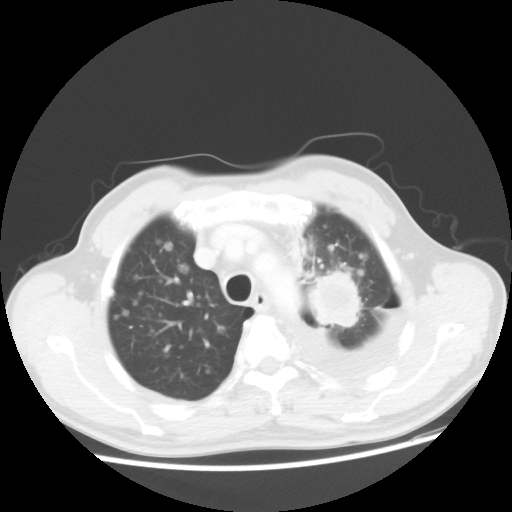
Chest CT, one axial slice. Slice 38 of 48 in the series (ordered by position). 100 kVp. Lung window (W 1500 / L -600 HU). 512 × 512 image matrix, field of view 362 × 362 mm. Patient: male, 55 years. From the clinical record (not read from this slice): clinical TNM (as recorded): T2 N3 M1a; histopathological grade: G3.
Outlined on this slice (rectangle marked by the reading radiologist):
- lung tumour (recorded histology: squamous cell carcinoma): bounding box (x1, y1, x2, y2) in pixels: (304, 258, 369, 338)